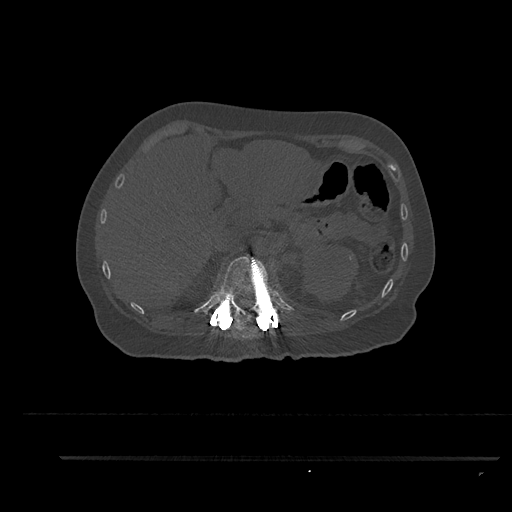
CT including the spine, one axial slice. Position 268 of 797 along the scan axis. Bone window (W 1800 / L 400 HU). 0.5 mm slice thickness. 512 × 512 image matrix, field of view 408 × 408 mm. Patient: female, 44 years. From the clinical record (not read from this slice): primary cancer: renal; vertebrae with lytic lesions (as recorded): L1.
Structures marked on this image (semi-automatically segmented with operator editing):
- T12 vertebra: bounding box (x1, y1, x2, y2) in pixels: (217, 255, 282, 328)